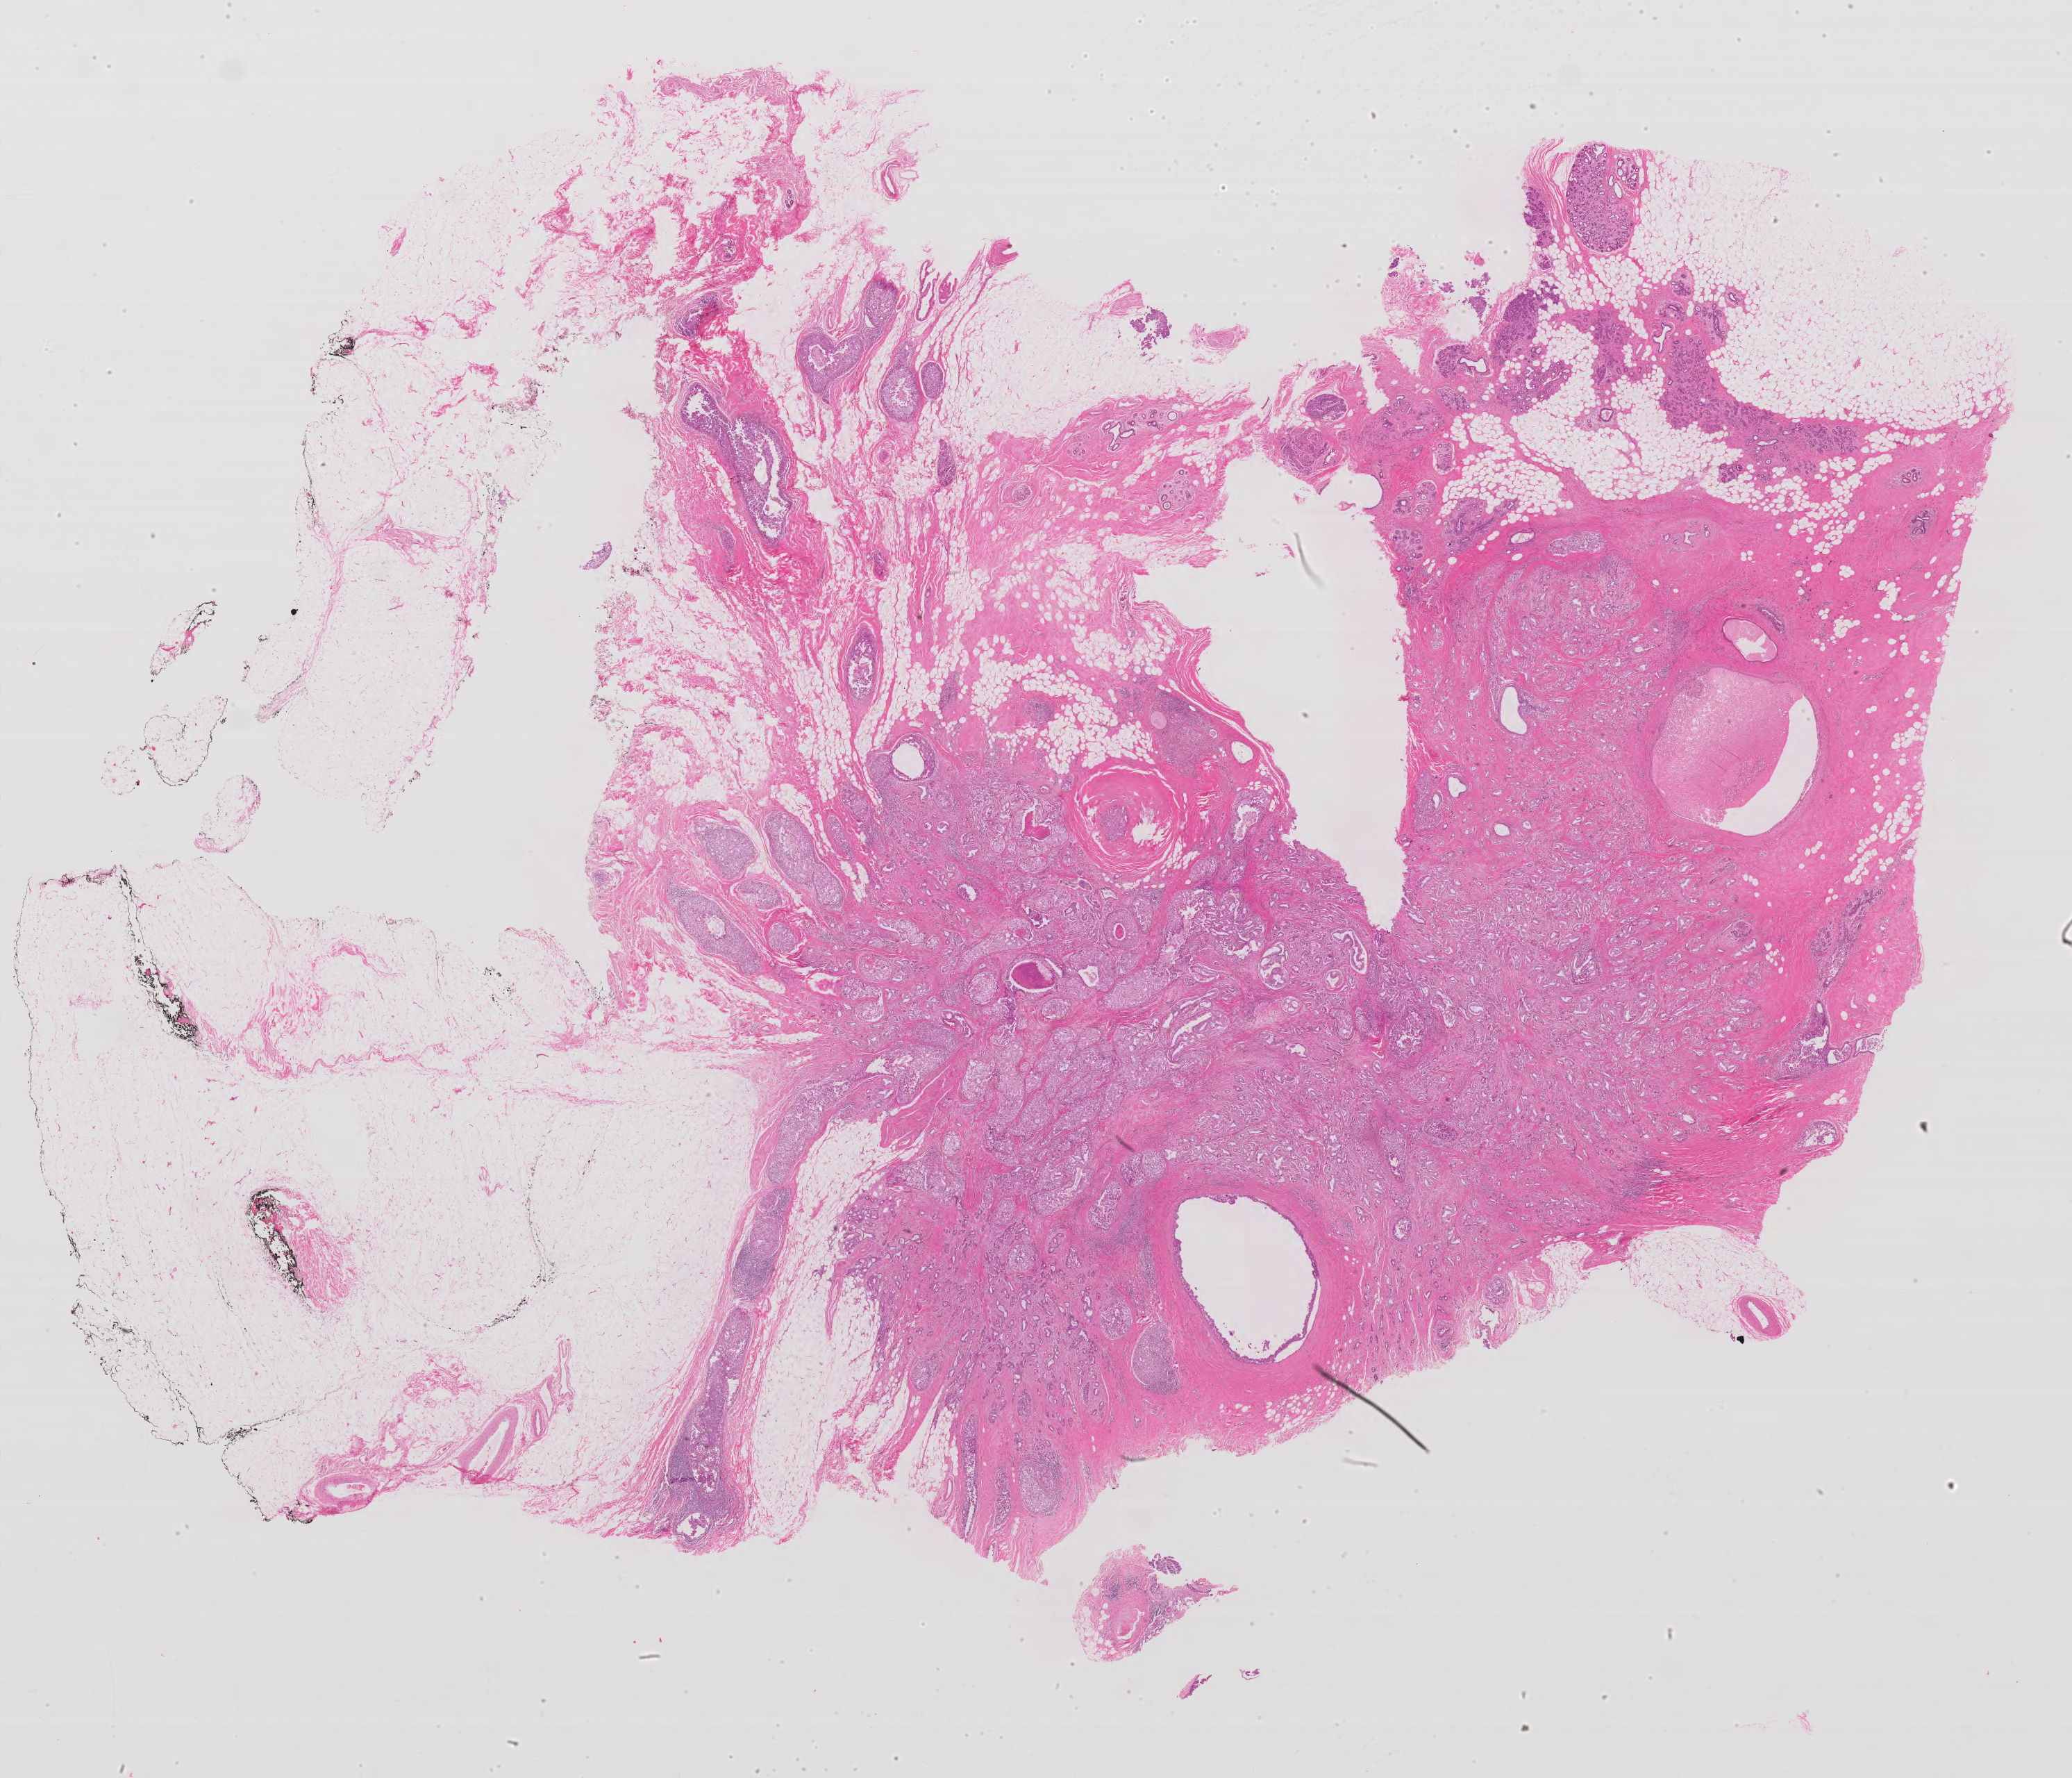
Digitized H&E tissue section (whole slide) — low-resolution overview of the scanned area, about 23.9 x 20.5 mm (from a 40x scan). Formalin-fixed paraffin-embedded (FFPE) diagnostic section. Primary tumour sample from the breast. Patient: female, age at initial diagnosis 52 years.
- AJCC pathologic stage: IA (7th edition)
- laterality: right
- diagnosis: Infiltrating duct carcinoma, NOS
- lymph nodes positive (case pathology): 0 of 2 examined